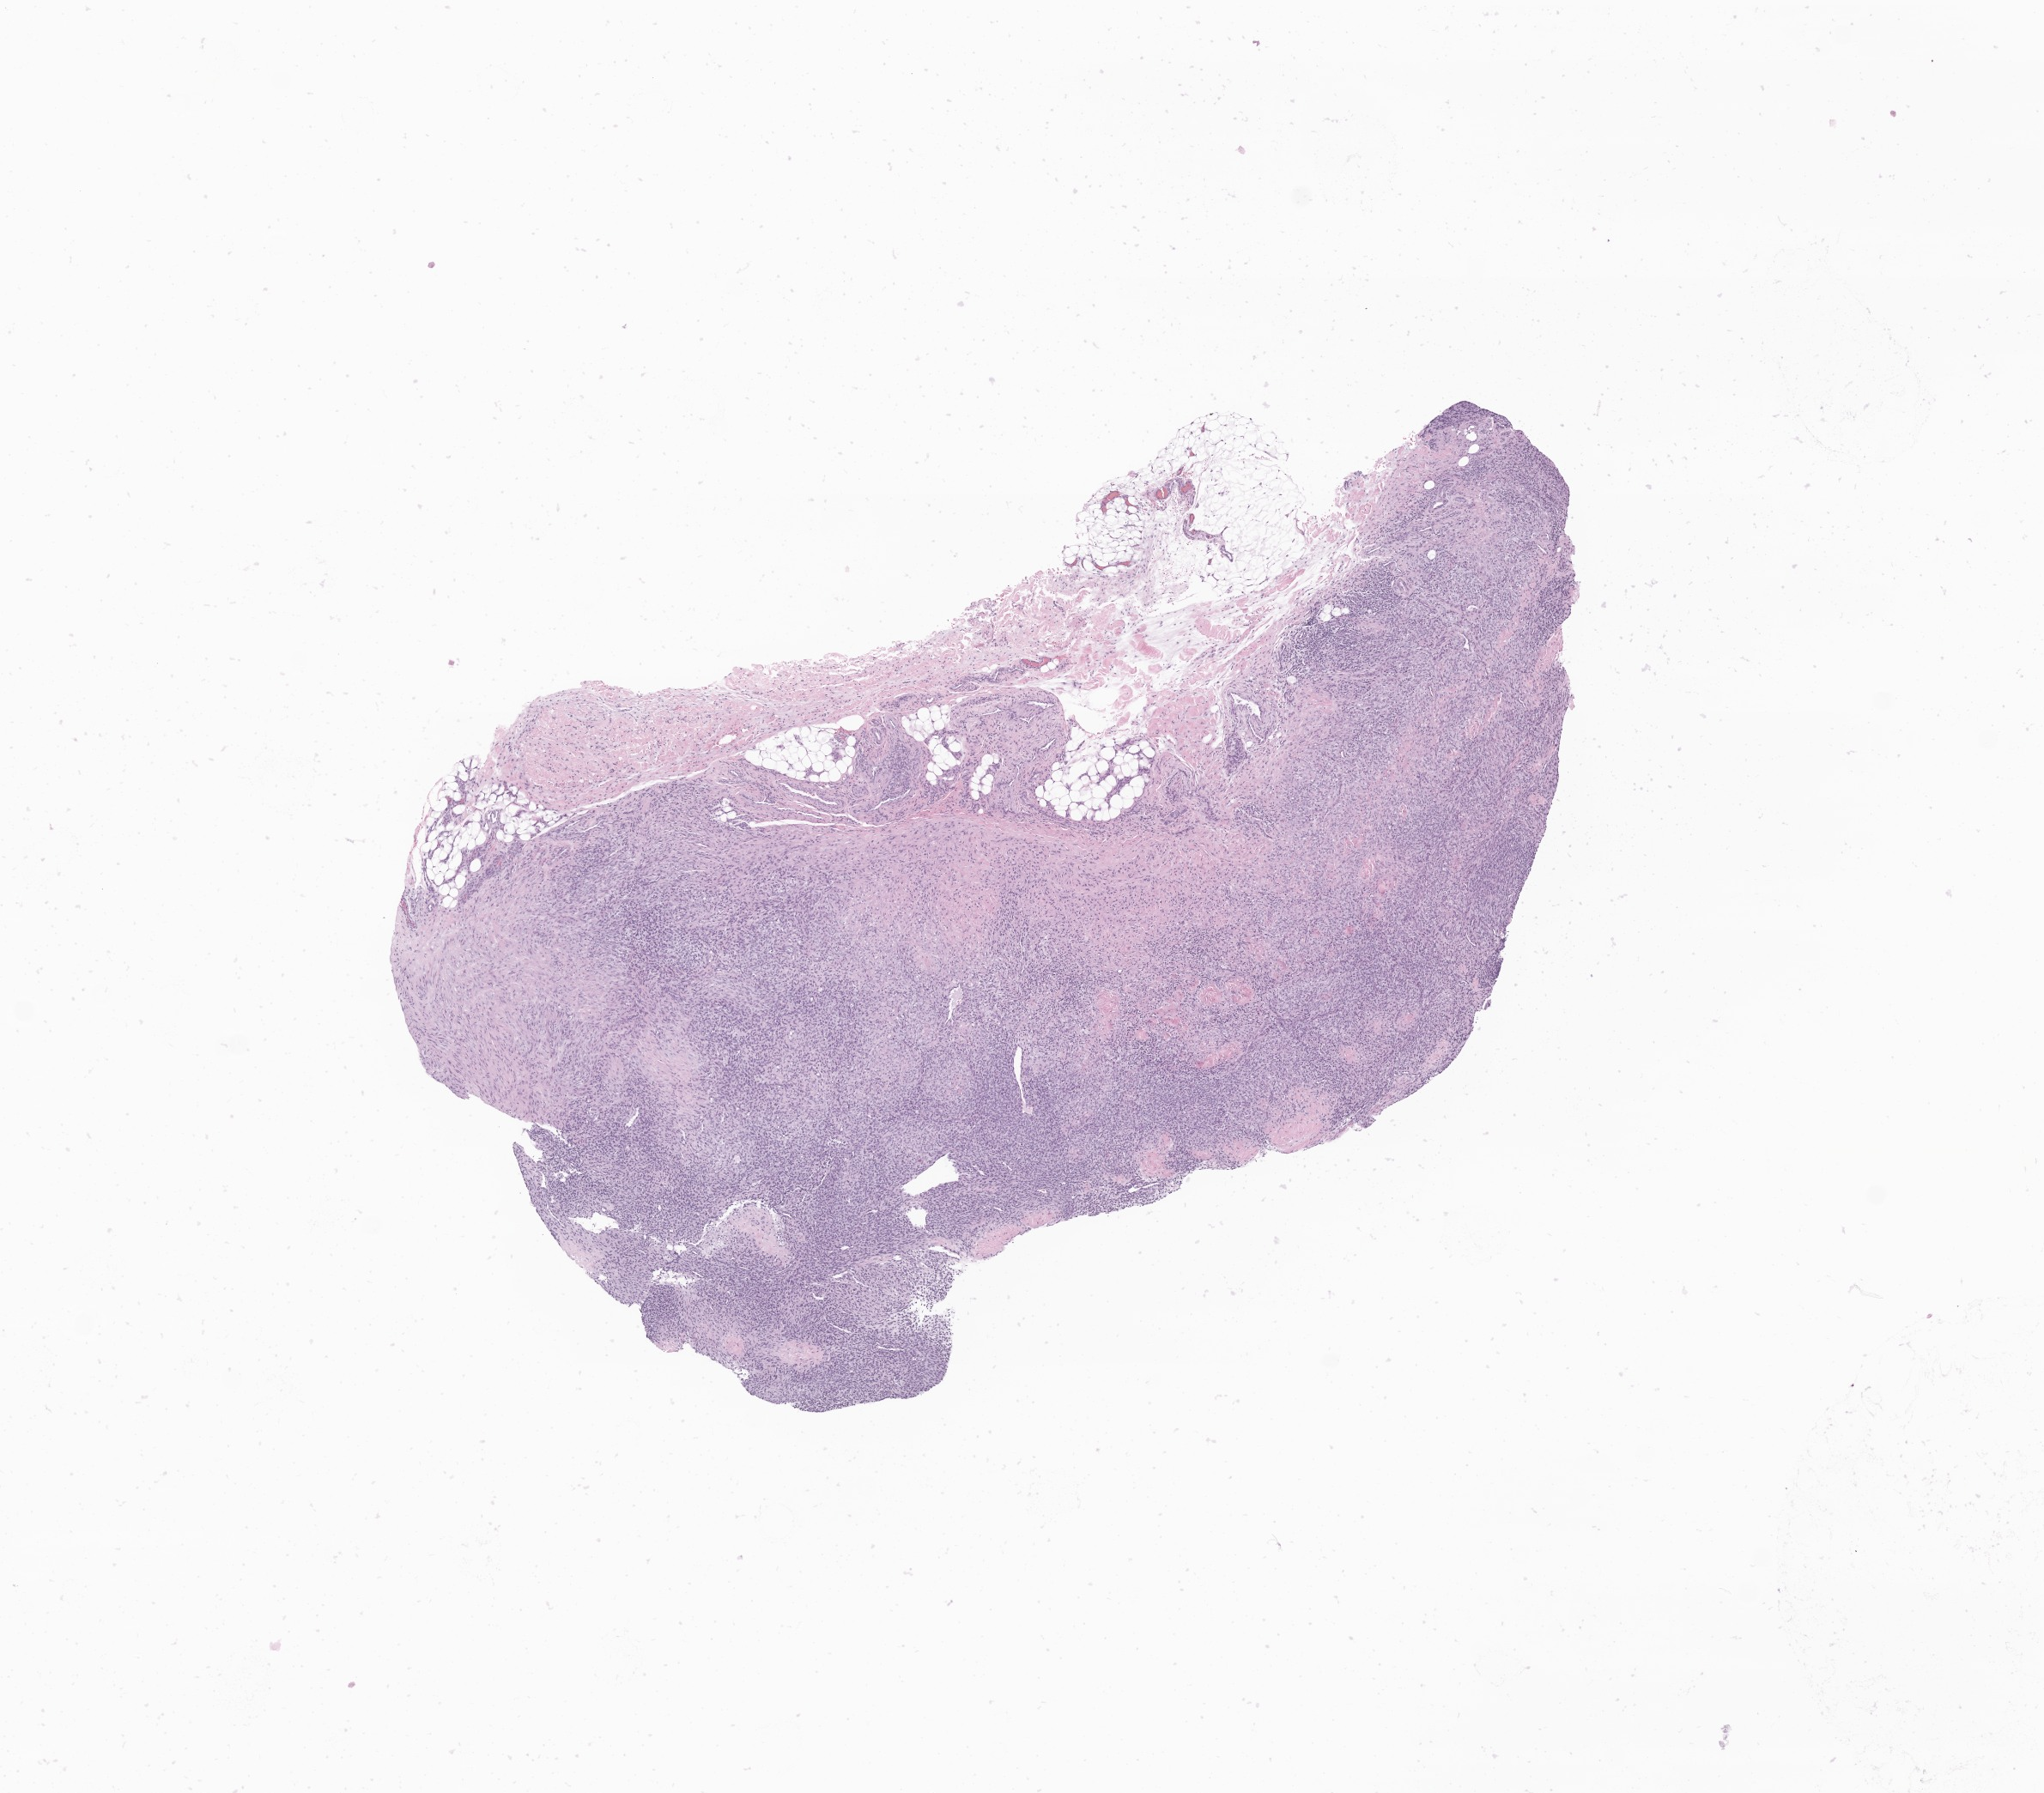
Haematoxylin and eosin whole-slide image of tumor tissue from the soft tissue of upper extremity — whole scanned area (about 10.0 x 8.8 mm) shown as a low-resolution overview; formalin-fixed, paraffin-embedded (FFPE) tissue. Patient female; age 110 days.
Recorded diagnosis: Infantile fibrosarcoma.